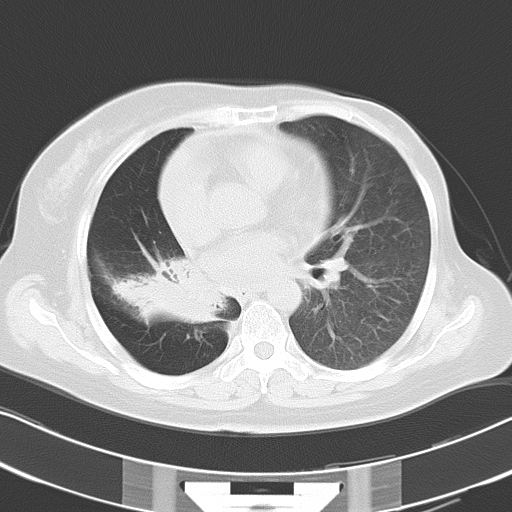
Chest CT, one axial slice; slice 16 of 30 in the series (ordered by position); lung window (W 1500 / L -600 HU); 8 mm slice thickness; 512 × 512 image matrix. Patient: female, 53 years. Case-level facts recorded for this patient, not image findings: clinical TNM (as recorded): T2b N1 M0.
Outlined on this slice (bounding box drawn by a radiologist):
- lung tumour (recorded histology: adenocarcinoma): box from (x=111, y=251) to (x=225, y=330) px